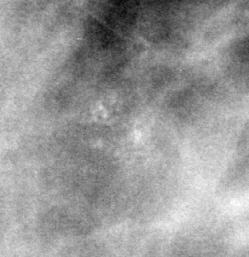
Region of interest cut from a scanned film mammogram (one marked finding); right breast; MLO view; BI-RADS breast density category 3 (scale 1–4).
Finding: calcifications, morphology pleomorphic, distribution clustered; BI-RADS assessment category 4; subtlety rating 3 on a 1 (subtle) to 5 (obvious) scale; pathology result (as recorded, not read from the image): benign.